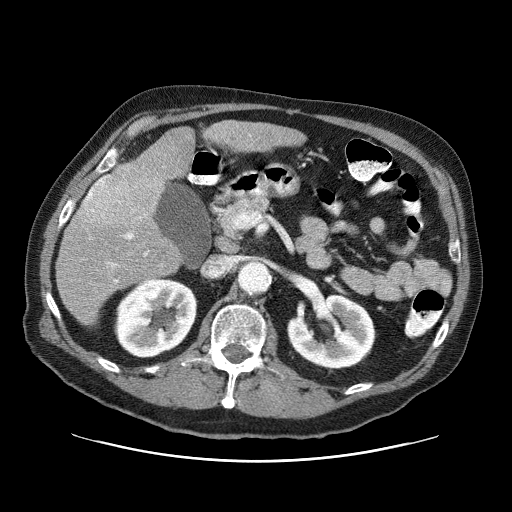
Contrast-enhanced abdominal CT (liver protocol), one axial slice; slice 31 of 87 in the series (ordered by position); reconstruction kernel STANDARD; 120 kVp; one of 3 acquisitions stored at this slice position; soft-tissue window (W 400 / L 40 HU); 512 × 512 image matrix, field of view 400 × 400 mm. Case-level facts recorded for this patient, not image findings: diagnosis: hepatocellular carcinoma (patient treated with transarterial chemoembolisation; whether this scan precedes or follows treatment is not stated here); TNM stage (as recorded): Stage-IIIA; Child-Pugh class: A.
Structures marked on this image (semi-automatic segmentation, software-assisted and operator-edited):
- liver parenchyma outside the tumour (the mass and vessels are separate outlines, so this box may not span the whole liver): bounding box <56,120,304,325> (left, top, right, bottom; pixels)
- mass: <78,161,163,233>
- liver vessels: <110,135,251,282>